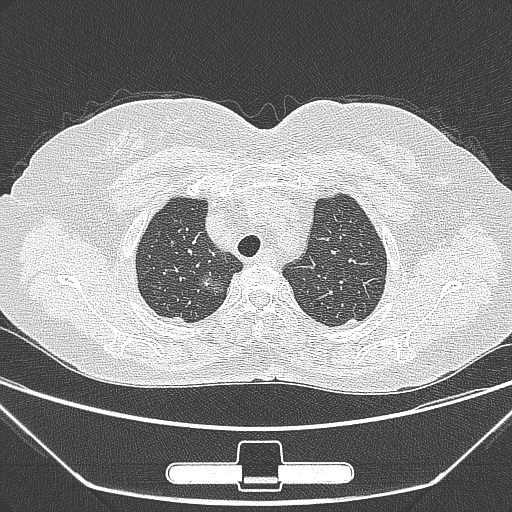
Chest CT, one axial slice; lung window (W 1500 / L -600 HU); 1 mm slice thickness; 512 × 512 image matrix, field of view 356 × 356 mm. Patient: female, 63 years. From the clinical record (not read from this slice): clinical TNM (as recorded): T1a N0 M0.
Outlined on this slice (bounding box drawn by a radiologist):
- lung tumour (recorded histology: adenocarcinoma): box from (x=194, y=268) to (x=231, y=303) px